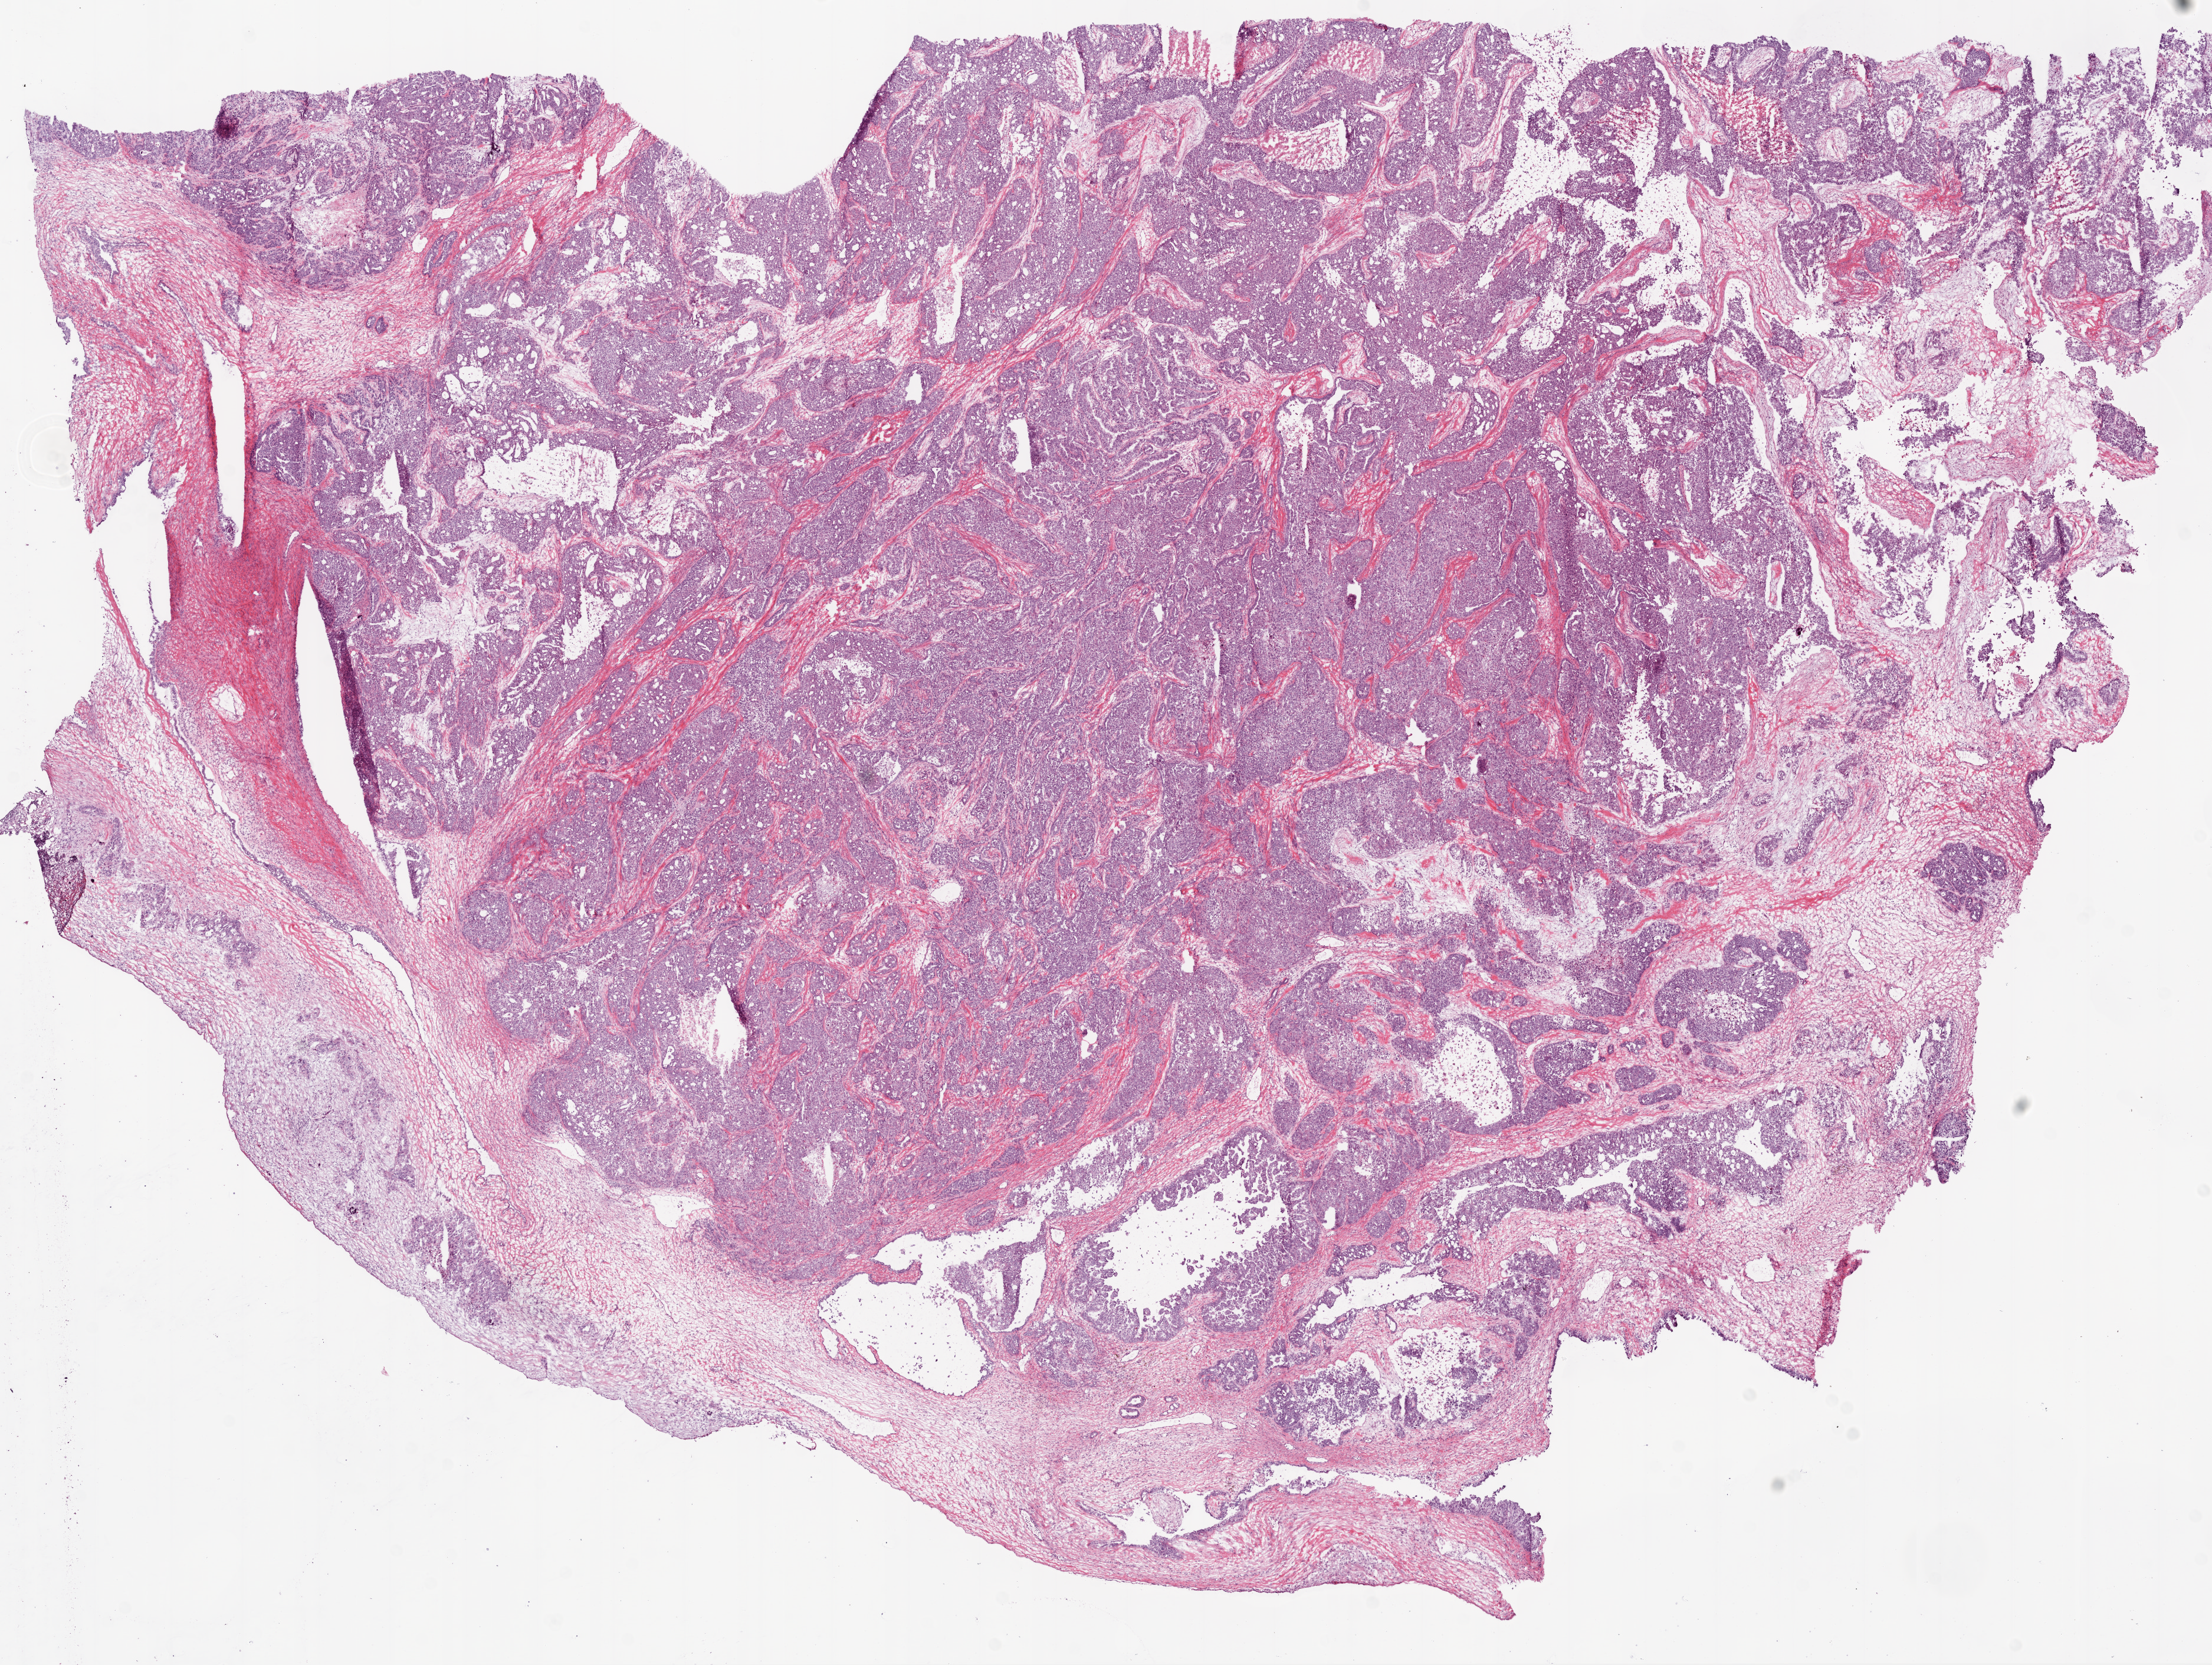
Whole-slide histology image, Hematoxylin and eosin (H&E) stained — low-resolution overview of the scanned area, about 15.0 x 11.3 mm (acquisition: 20x scan); frozen section from the bottom of the tissue portion; primary tumour sample from the ovary. Female patient; age at initial diagnosis 73 years. Histologic grade: G3 (poorly differentiated). Pathologist review of this section (percent, as recorded): tumour cells 90%, tumour nuclei 95%, normal cells 0%, stromal cells 10%, necrosis 0%.
* laterality: bilateral
* histologic diagnosis: Serous cystadenocarcinoma, NOS
* FIGO stage: IIIC